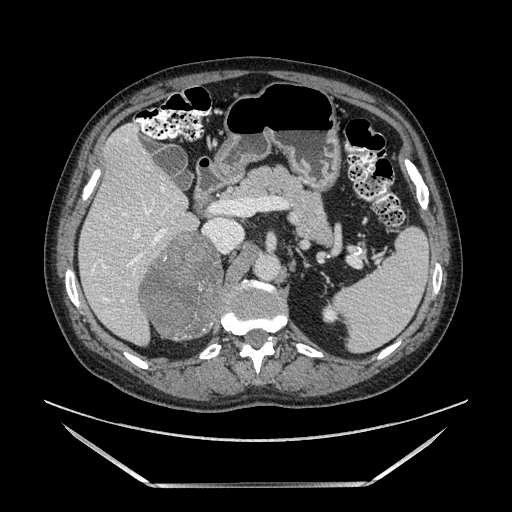
Contrast-enhanced abdominal CT, one axial slice. Slice 85 of 185 in the series (ordered by position). Soft-tissue window (W 400 / L 40 HU). 512 × 512 image matrix, field of view 440 × 440 mm. Male patient. Case-level facts recorded for this patient, not image findings: diagnosis: adrenocortical carcinoma; tumour side: right adrenal; tumour size at pathology: 10.3 cm; Ki-67 index: 20 %; stage (as recorded): 3.
Annotated regions visible in this slice (semi-automatic segmentation, software-assisted and operator-edited):
- mass: bounding box <145,234,223,339> (left, top, right, bottom; pixels)